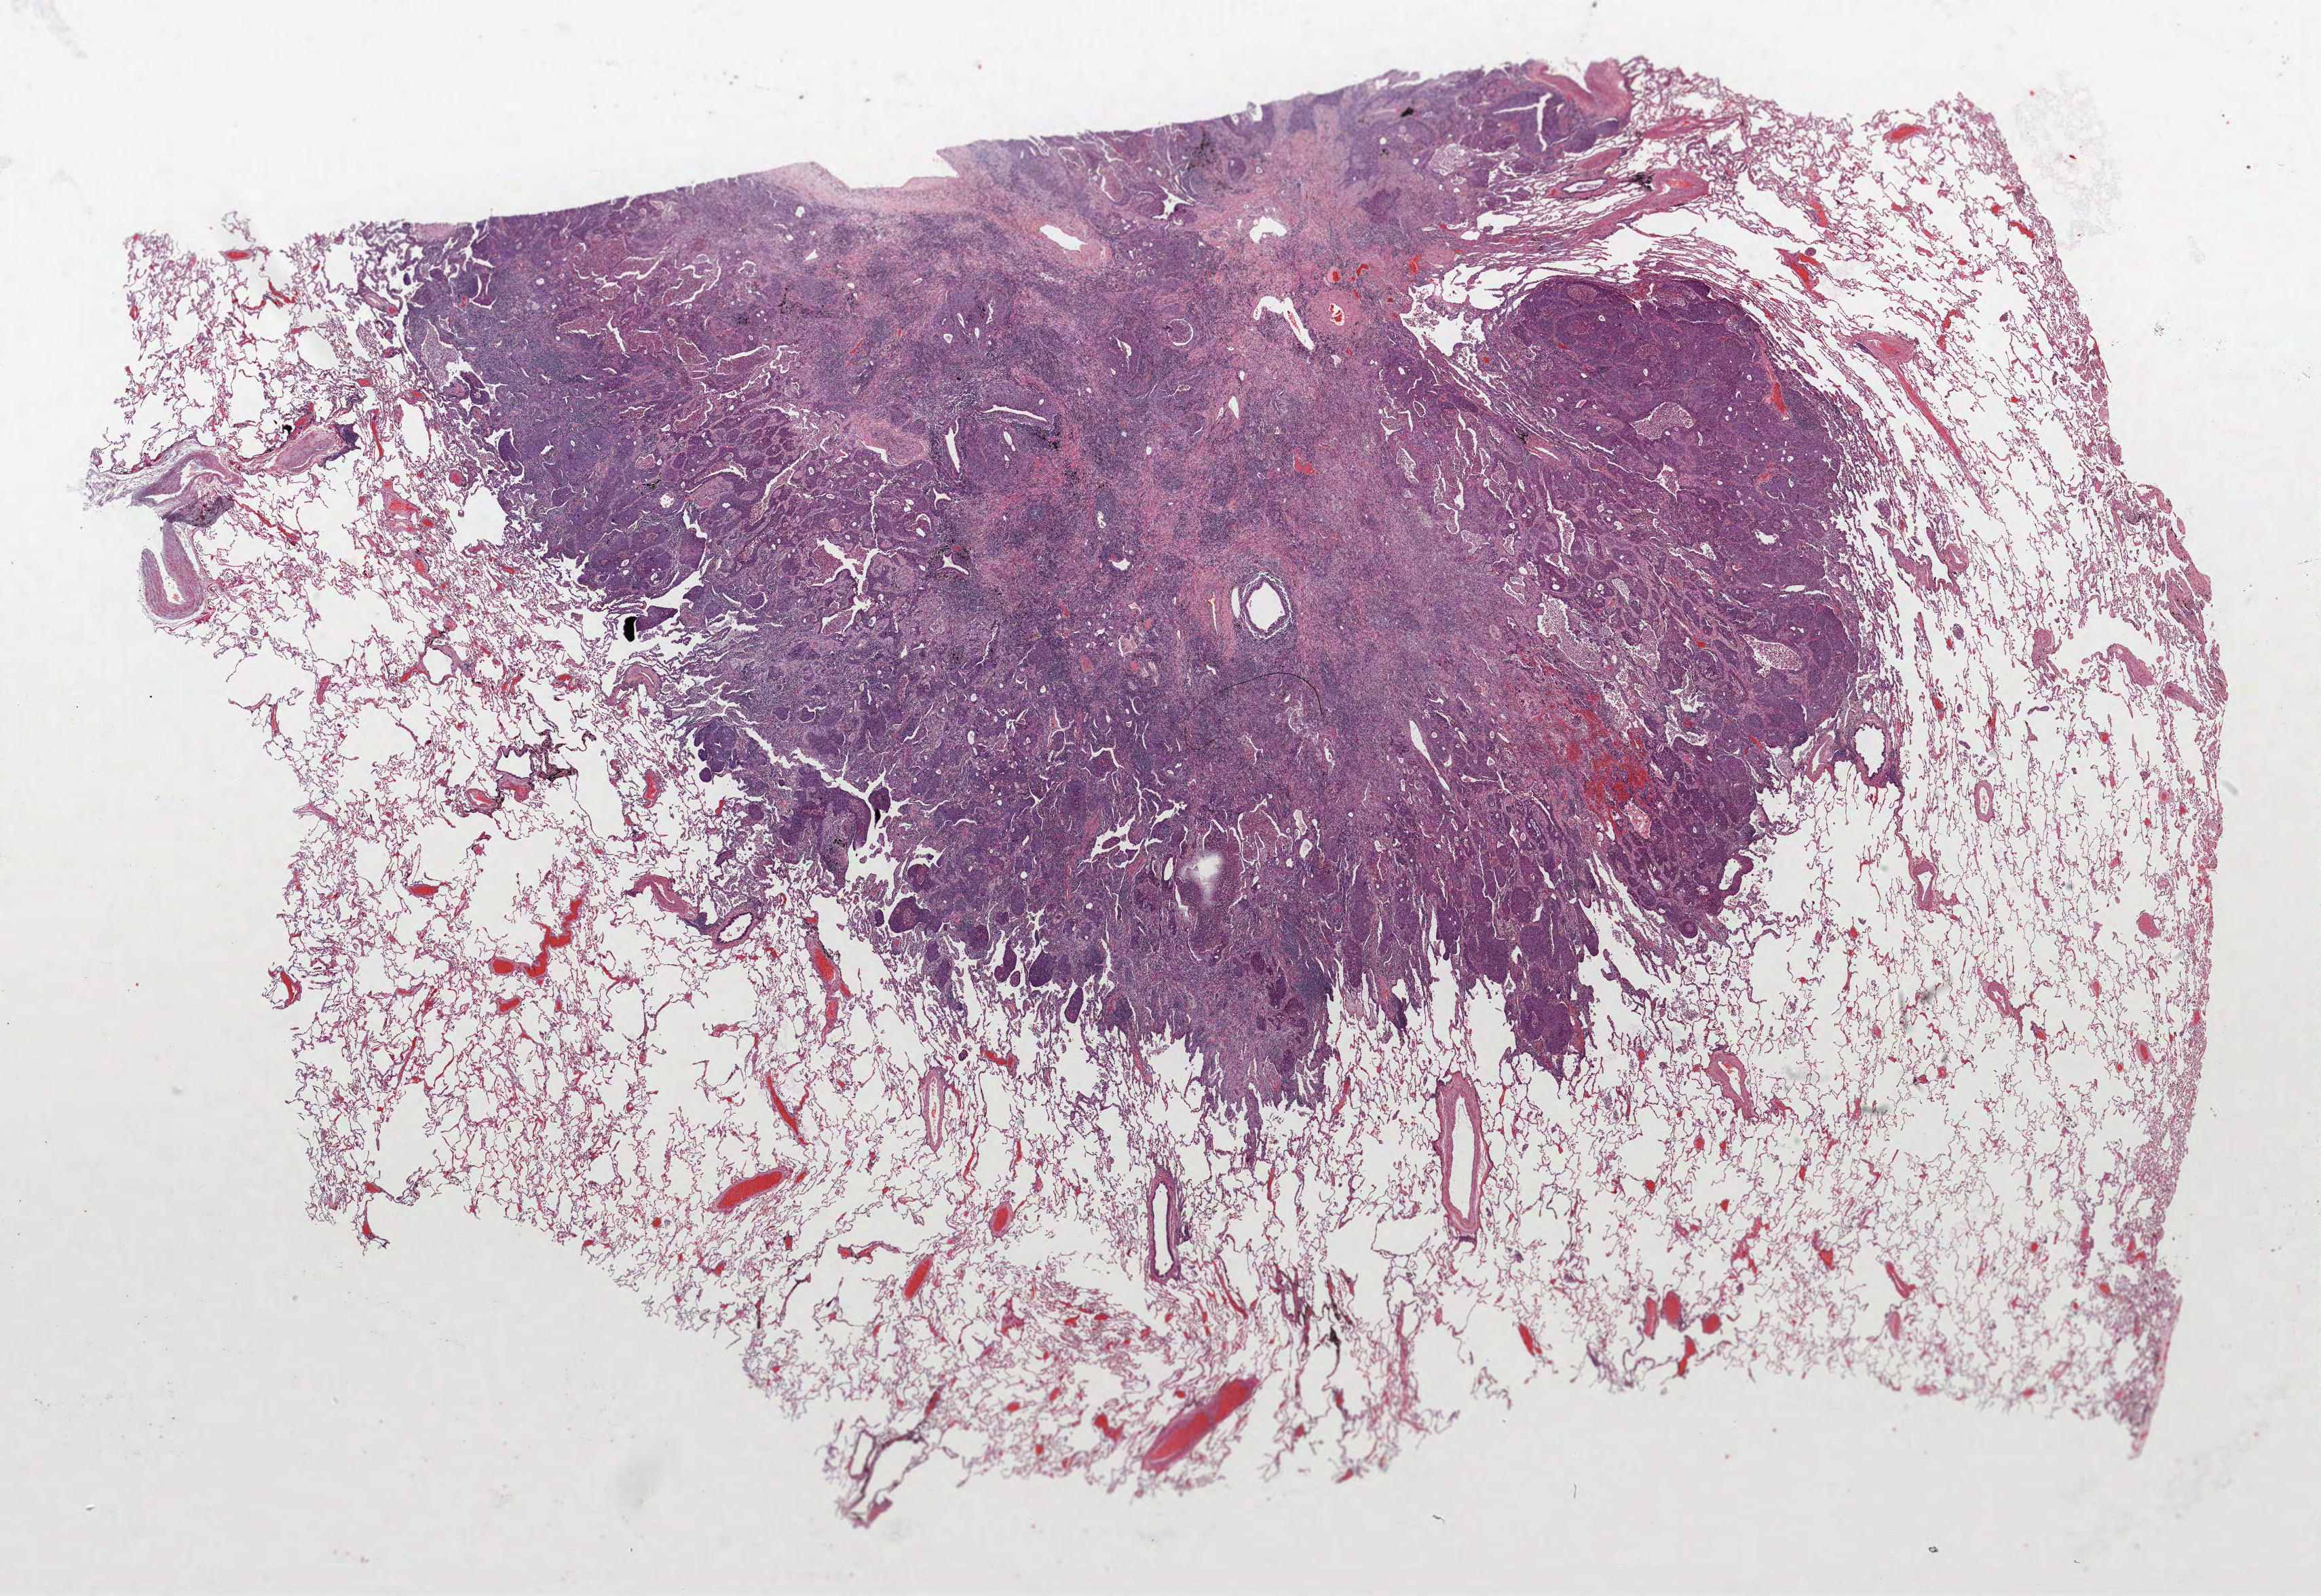
H&E-stained whole-slide image — low-resolution overview of the scanned area, about 27.4 x 18.8 mm, FFPE section, lung tissue. Male, age 68 at enrolment. Current smoker at enrolment. Grade: moderately differentiated (G2).
• tumour size (pathology): 25 mm
• primary tumour location (clinical record): left upper lobe
• participant's lung-cancer diagnosis: Squamous cell carcinoma, NOS (ICD-O-3 8070/3)
• stage (AJCC 6th edition): IIA